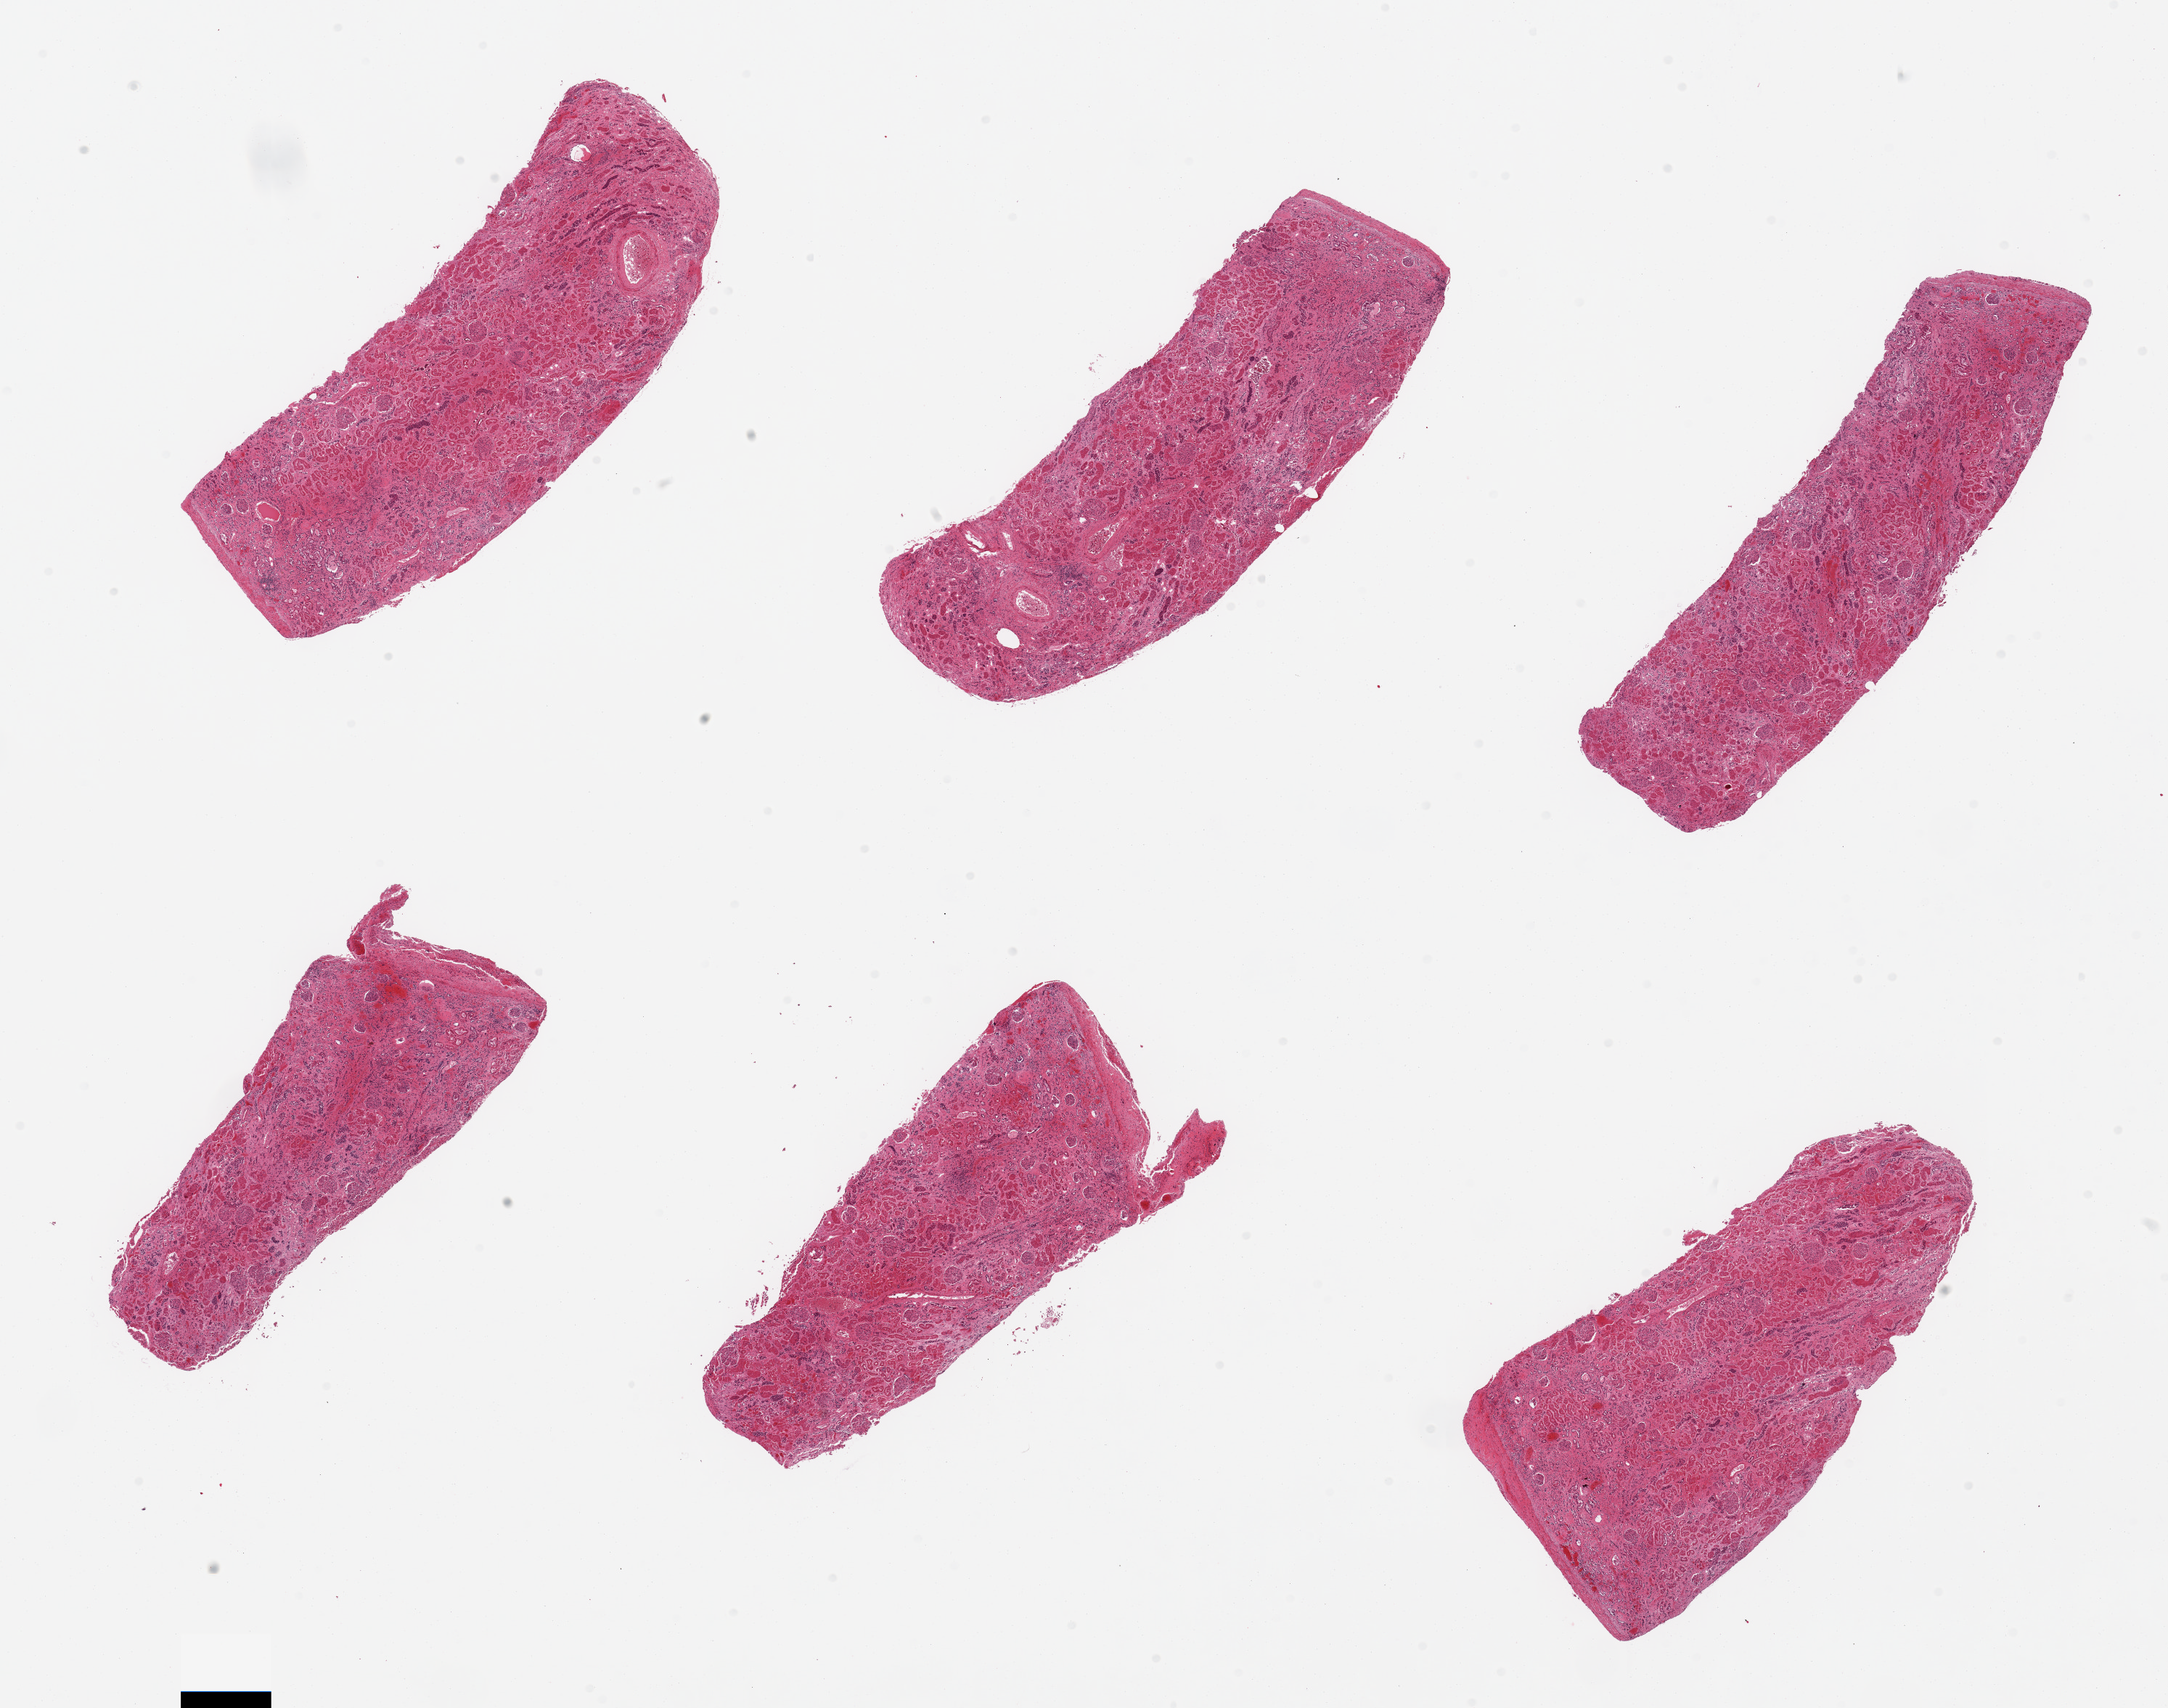
Hematoxylin and eosin (H&E) whole-slide image — low-resolution overview of the scanned area, about 23.6 x 18.6 mm, PAXgene-fixed, paraffin-embedded tissue, section of renal cortex (target tissue), tissue donor sample.
• pathologist's review note for this sample: 6 pieces; tubules totally autolyzed; glomeruli intact without lesions